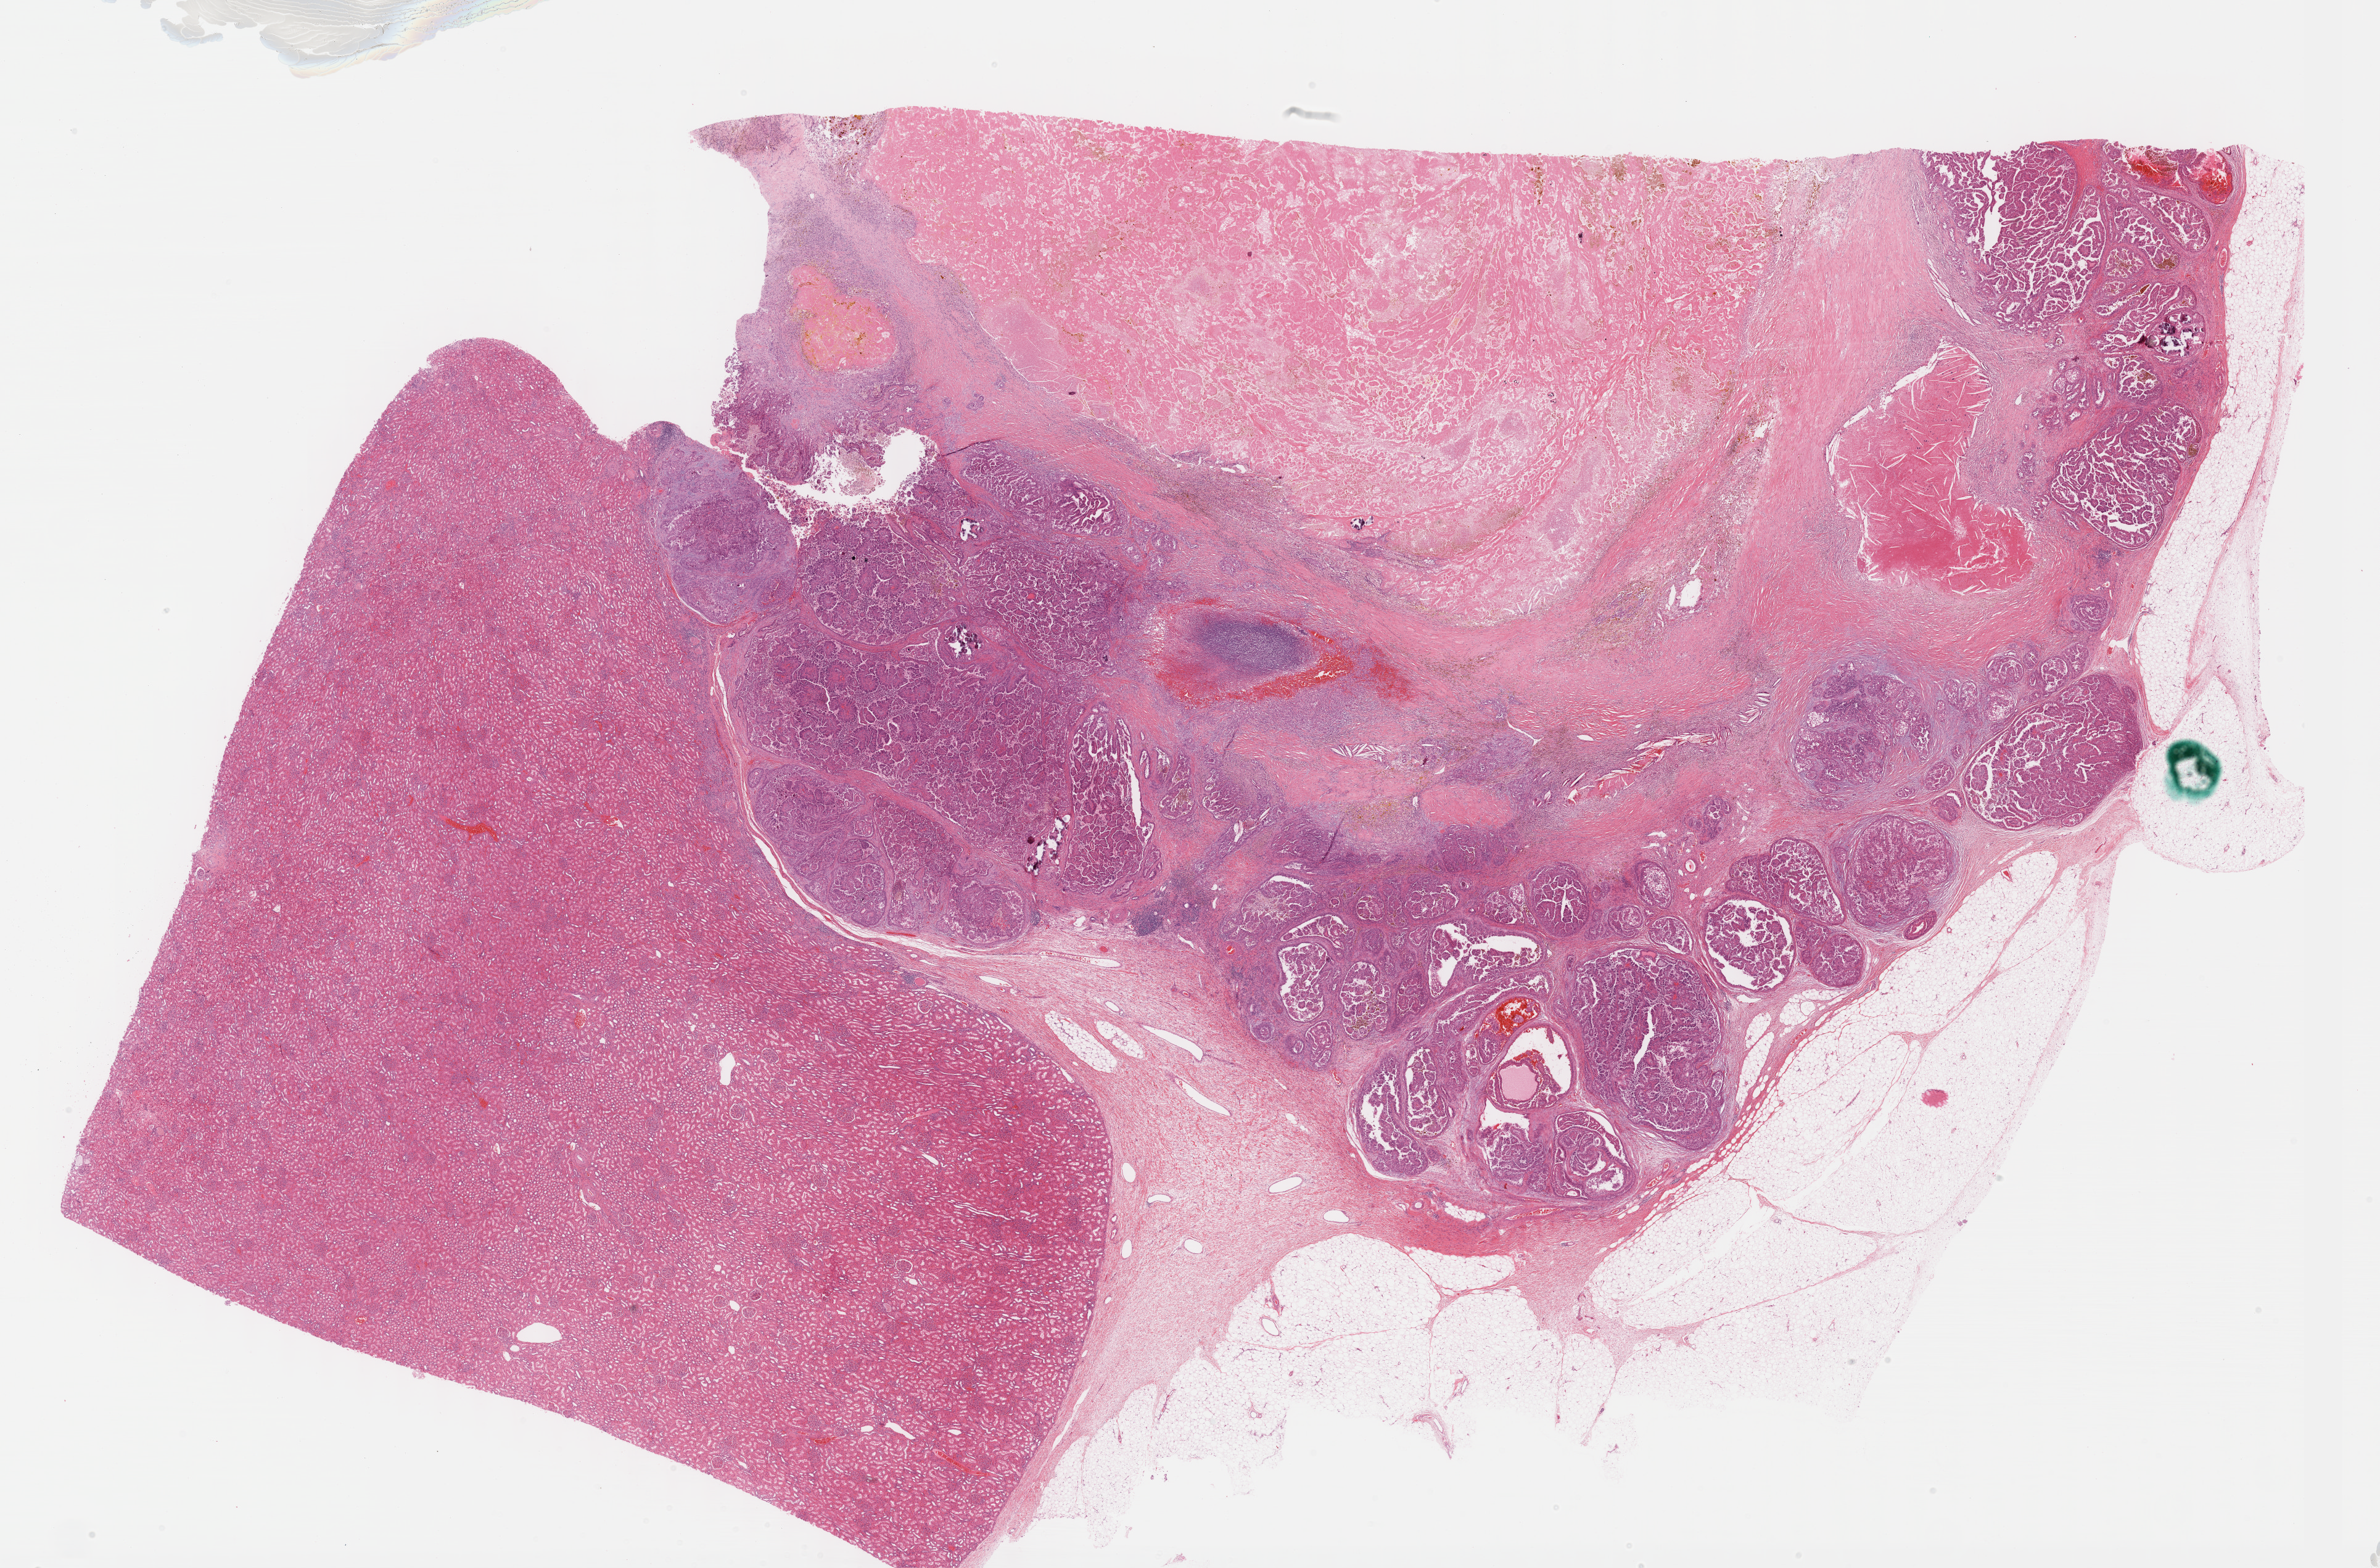
Whole-slide histology image, Hematoxylin and eosin (H&E) stained — low-resolution overview of the scanned area, about 31.2 x 20.5 mm; FFPE section; kidney, primary tumour sample. Male patient; age at initial diagnosis 54 years.
TNM: T3 NX MX. AJCC pathologic stage: III (6th edition). Laterality: left. Diagnosis: Papillary adenocarcinoma, NOS.